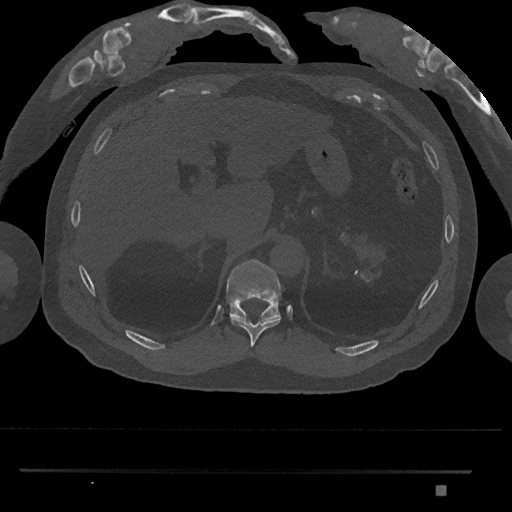
CT including the spine, one axial slice. Slice 975 of 1134 in the series (ordered by position). 120 kVp. Bone window (W 1800 / L 400 HU). 512 × 512 image matrix, field of view 429 × 429 mm. Male patient, age 65 years. Case-level facts recorded for this patient, not image findings: primary cancer: prostate.
Annotated regions visible in this slice (semi-automatically segmented with operator editing):
- T10 vertebra: bounding box <231,317,281,348> (left, top, right, bottom; pixels)
- T11 vertebra: <225,259,282,319>